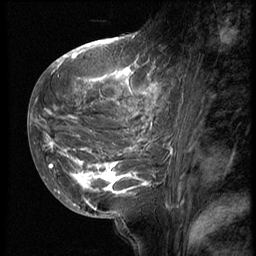
Breast MRI (dynamic contrast-enhanced), one sagittal slice. Position 23 of 62 along the scan axis. 3 images stored at this slice position (order not interpretable as contrast timing). 1.5 T. TE 4.2 ms, TR 9 ms. 2.5 mm slice thickness. 256 × 256 image matrix. Patient: female, 28 years. From the clinical record (not read from this slice): setting: breast cancer imaged before/during neoadjuvant chemotherapy.
Outlined on this slice (semi-automatically segmented with operator editing):
- analysis volume of interest (the breast-tissue region the enhancement analysis was run in; not a lesion): bounding box (x1, y1, x2, y2) in pixels: (42, 45, 170, 207)
- tumour enhancement mask (voxels above the 140 % enhancement threshold inside the analysis volume of interest): (42, 45, 161, 202)